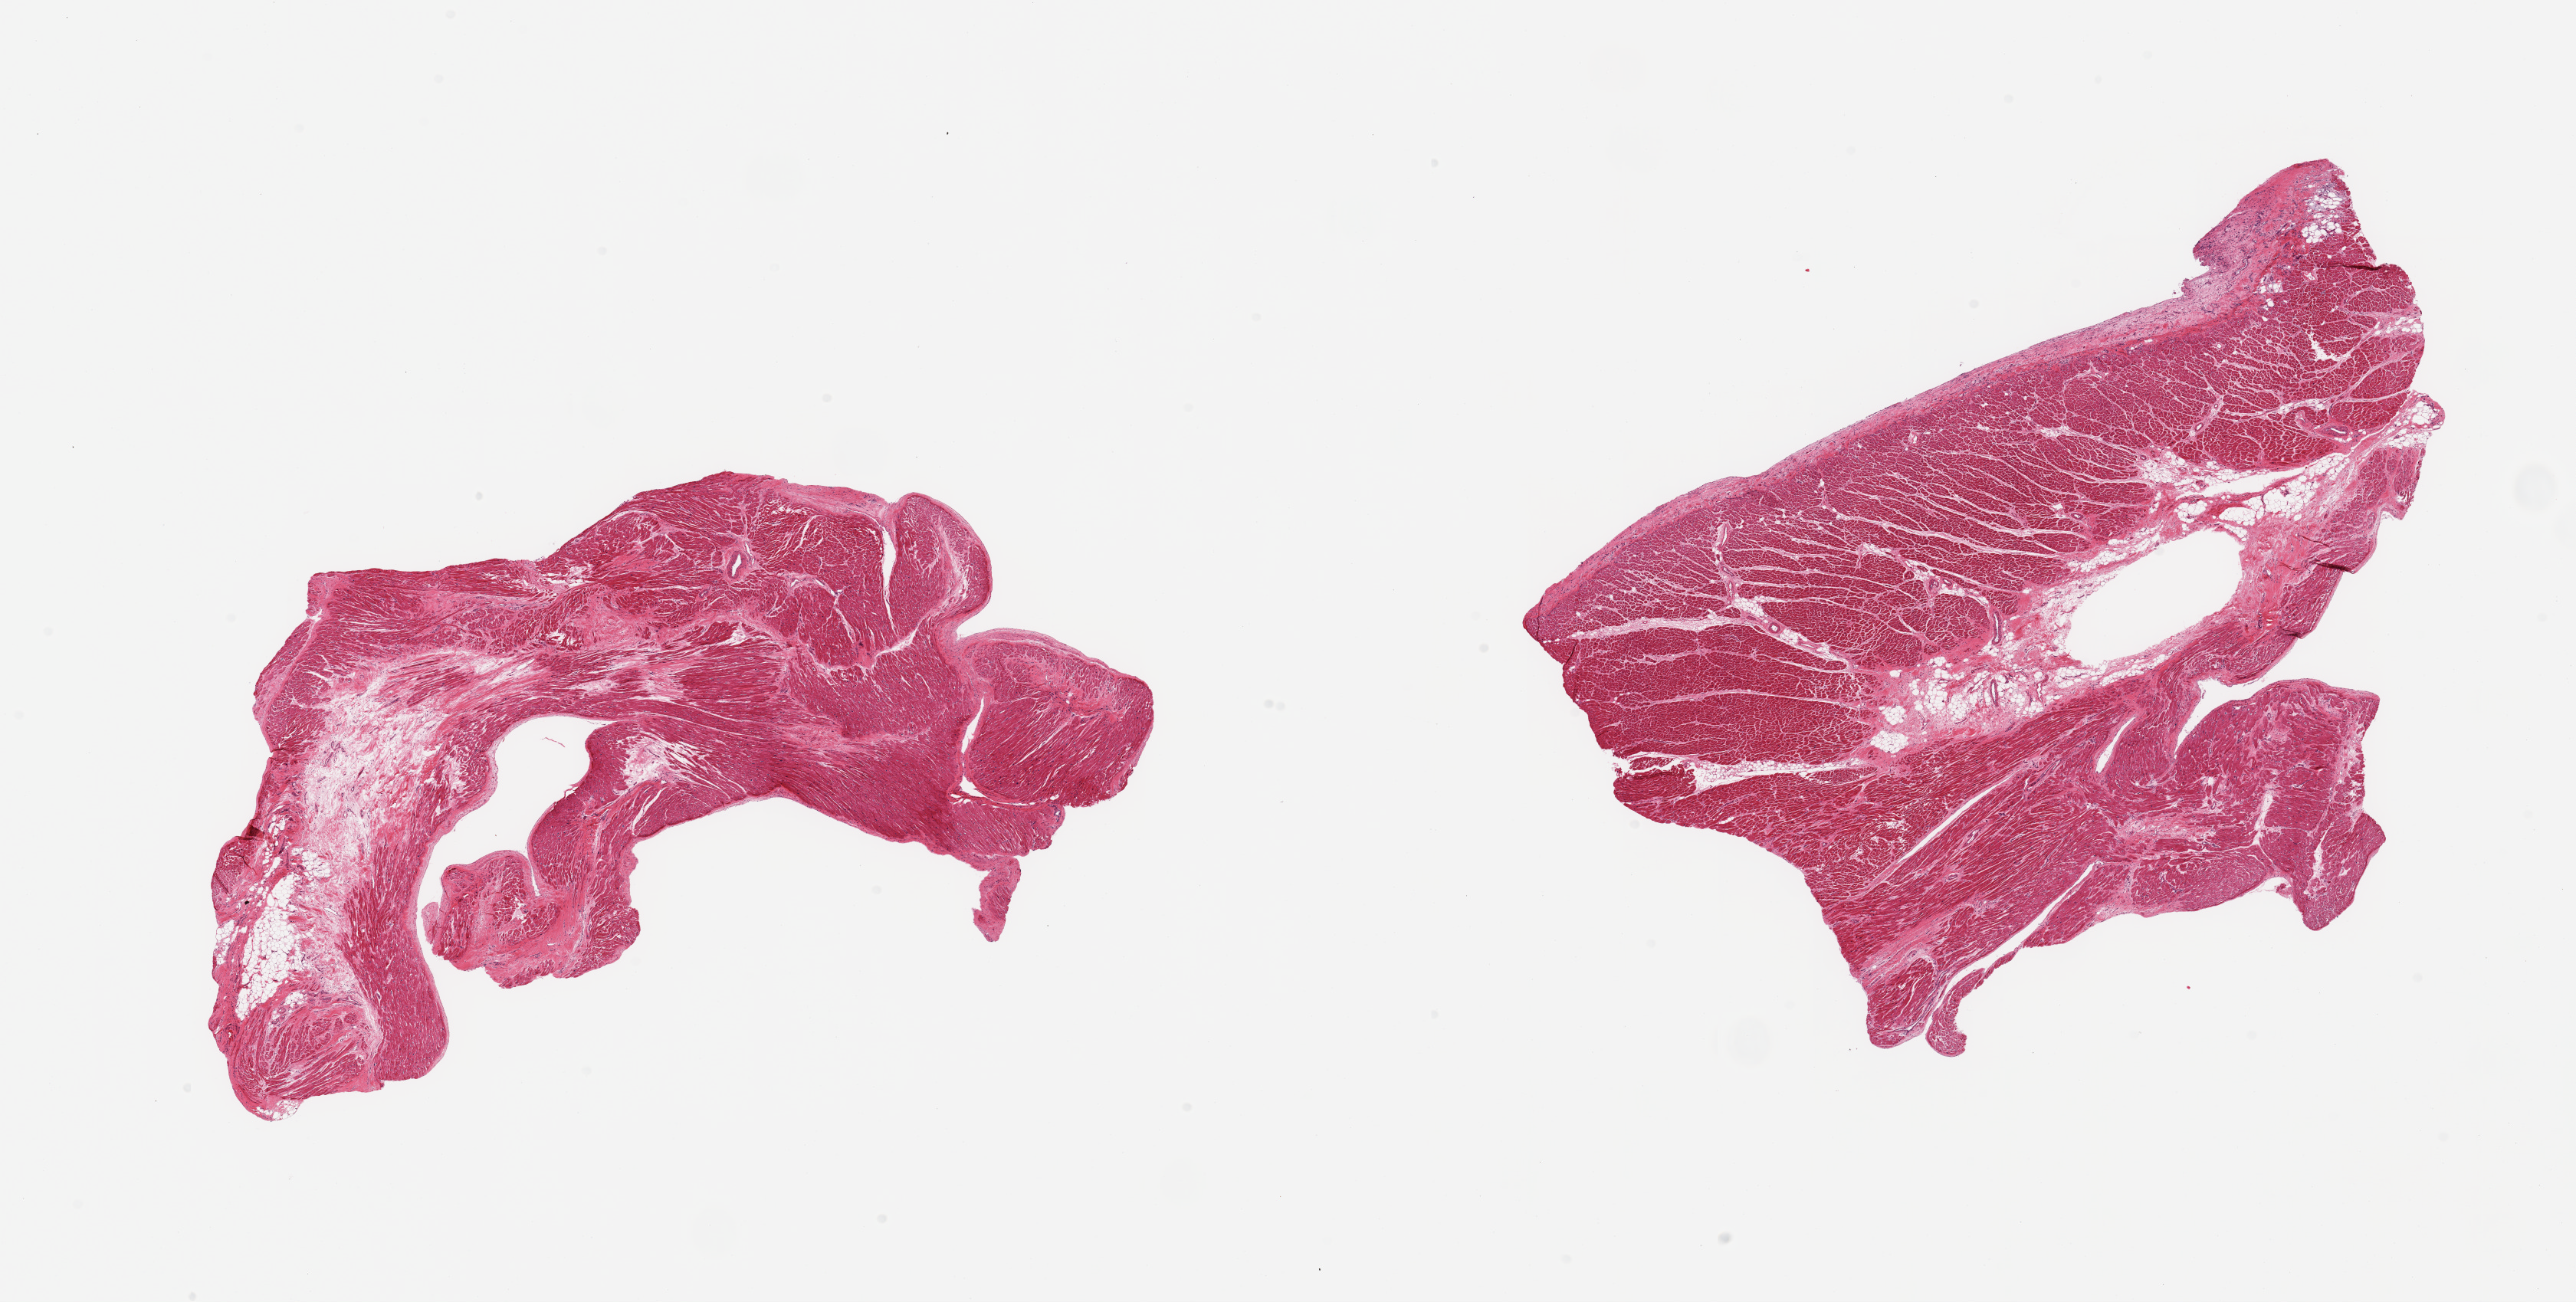
Whole-slide image, haematoxylin and eosin stain, low-resolution overview of the scanned area, about 26.6 x 13.4 mm (slide scanned at 20x); PAXgene-fixed, paraffin-embedded tissue; target tissue: heart; donor tissue sample. Donor sex: male.
Review note (as recorded): 22 pieces; patchy fibrosis (scars) up to 10% content.